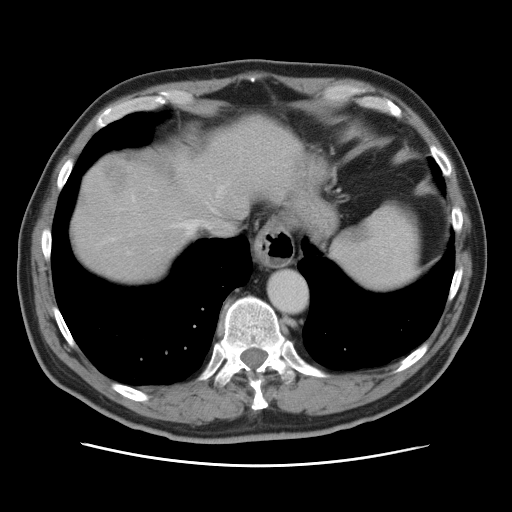
Contrast-enhanced abdominal CT, one axial slice. Position 68 of 80 along the scan axis. Intravenous contrast given. Soft-tissue window (W 400 / L 40 HU). 512 × 512 image matrix, field of view 370 × 370 mm. Male patient, age 69 years. Case-level facts recorded for this patient, not image findings: diagnosis: colorectal cancer liver metastases, imaged before liver resection; multiple liver metastases: no; largest metastasis: 5 cm; disease in both lobes: yes.
Outlined on this slice (manually delineated by an expert):
- hepatic veins: bounding box <130,185,225,235> (left, top, right, bottom; pixels)
- liver: <72,115,297,283>
- planned liver remnant (the part of the liver to remain after resection): <72,115,297,284>
- liver metastasis: <101,162,132,195>